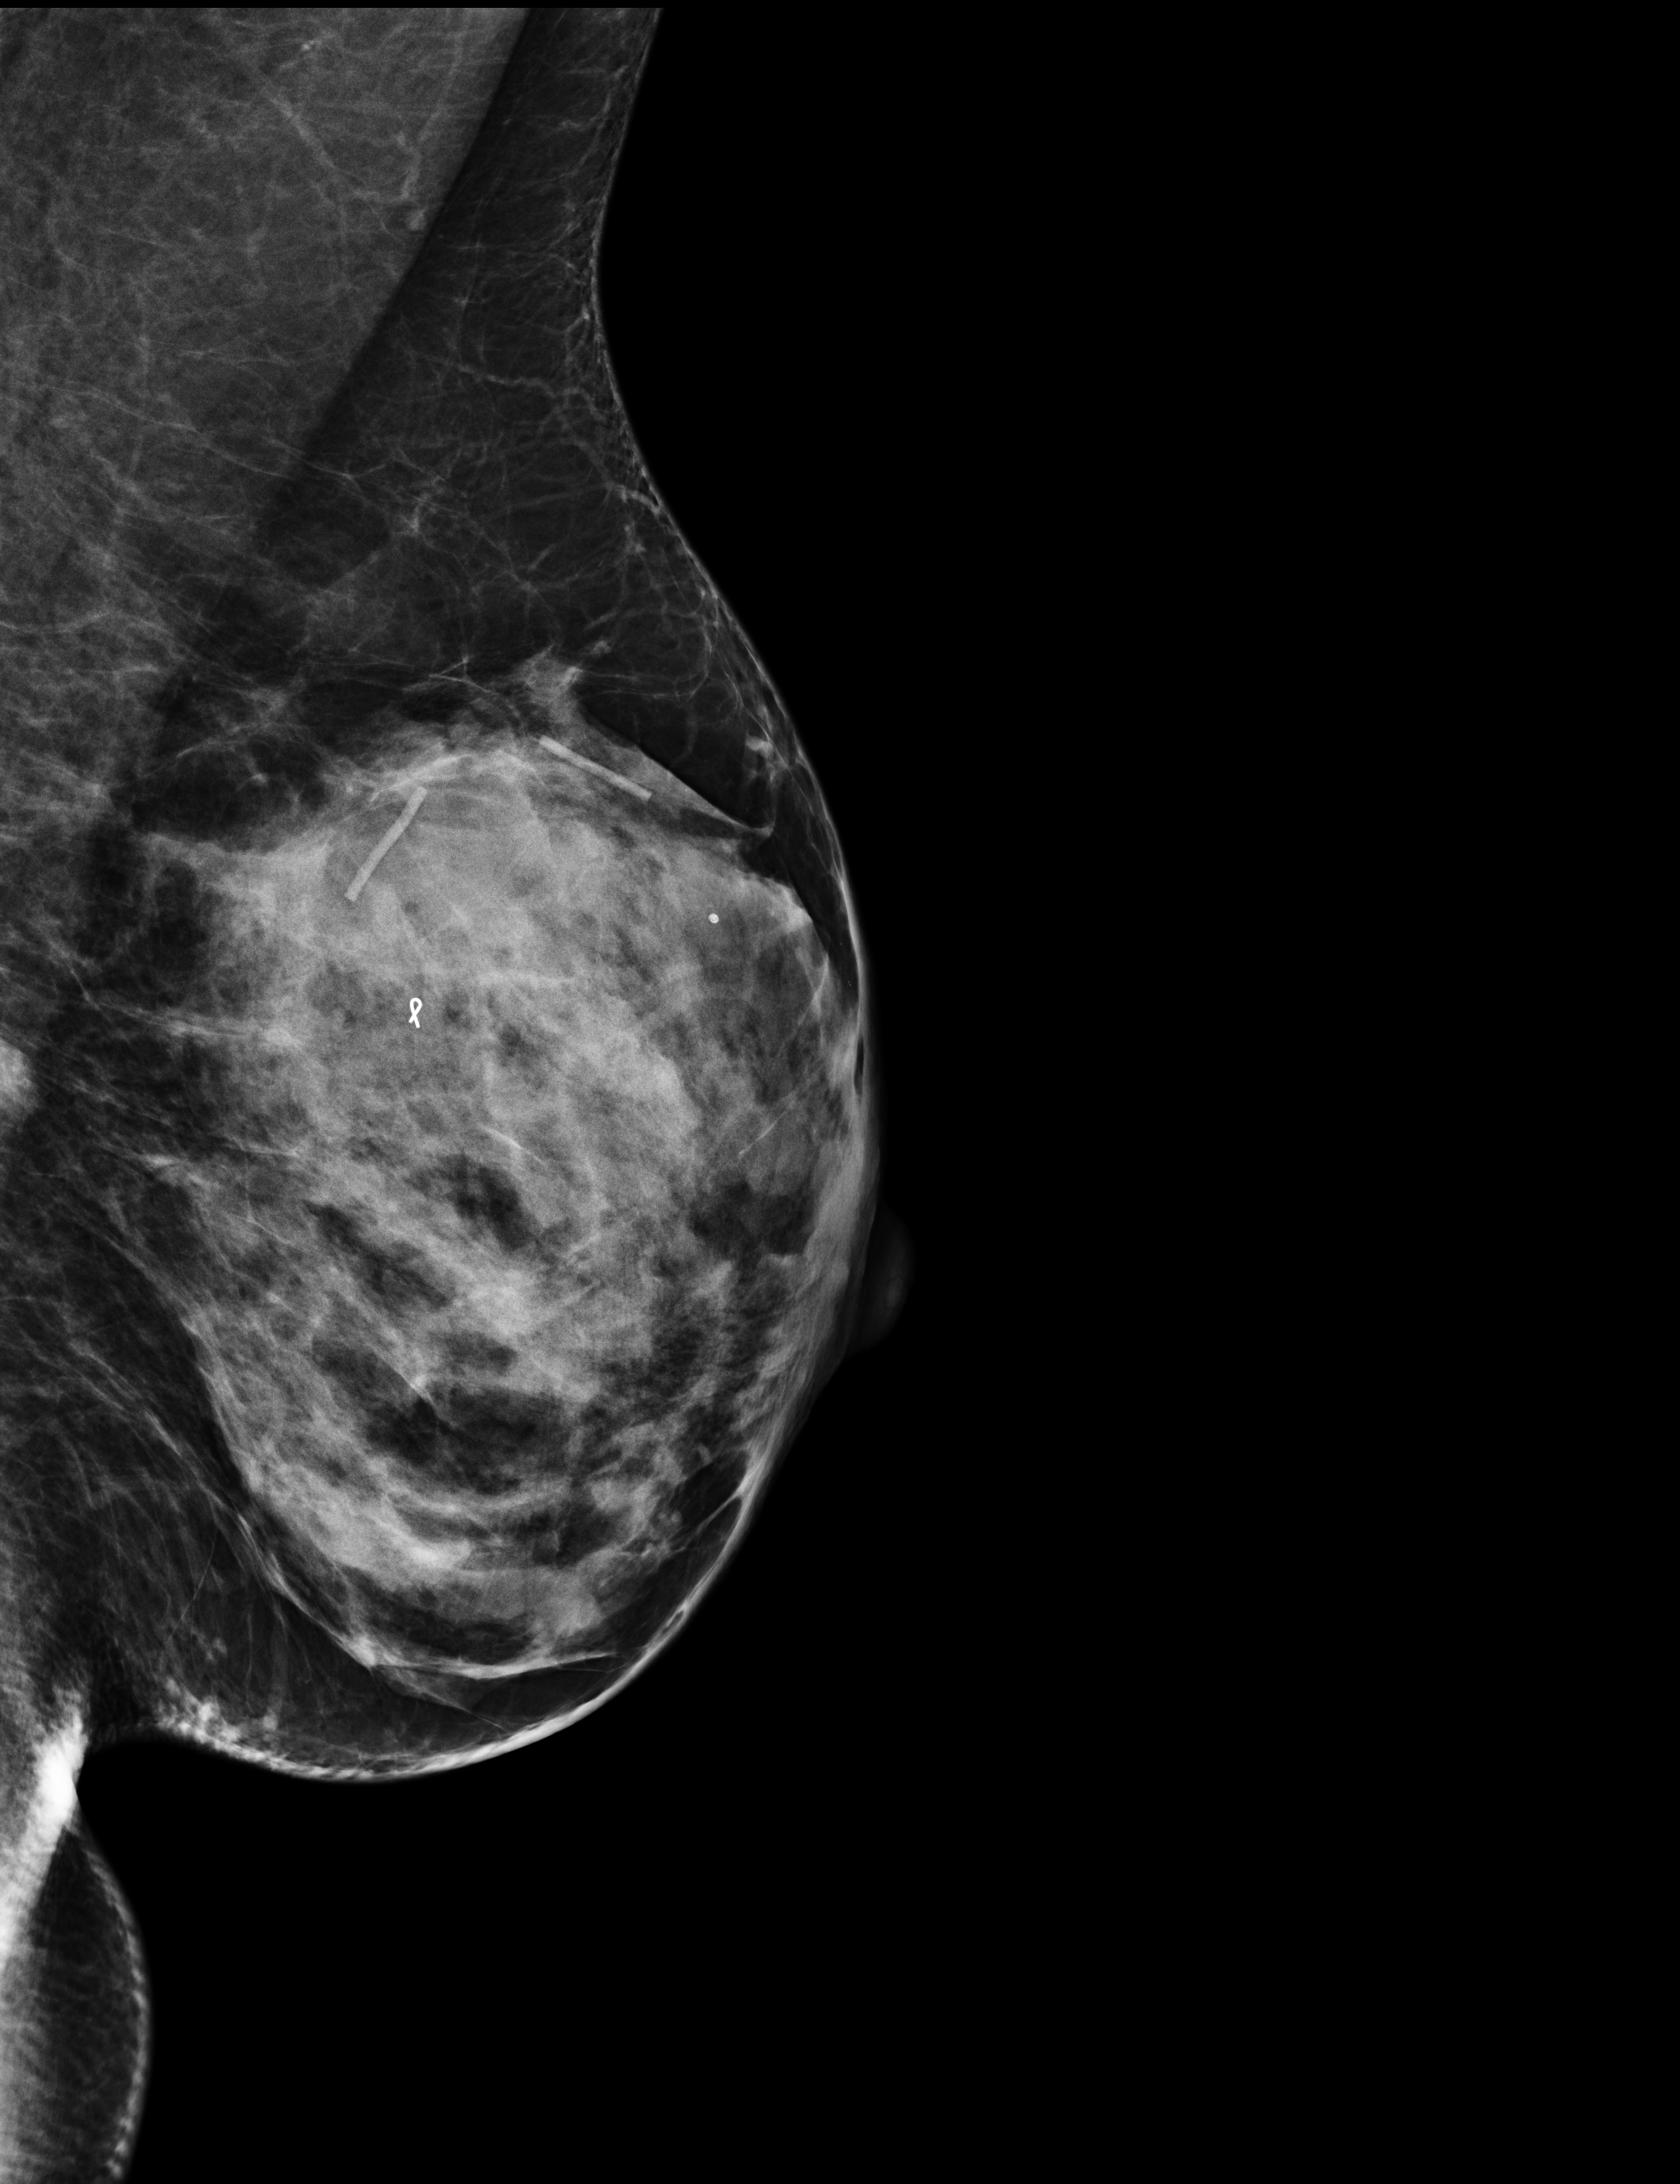
Digital mammogram (FFDM); left breast; medio-lateral oblique projection; screening examination; system: Selenia Dimensions. Patient: female, 47 years.
Breast density at the screening exam (both breasts): heterogeneously dense (BI-RADS density category c). Final BI-RADS category for the screening round (tomosynthesis exam, both breasts): category 4. Recall: recalled for additional imaging after this screen.